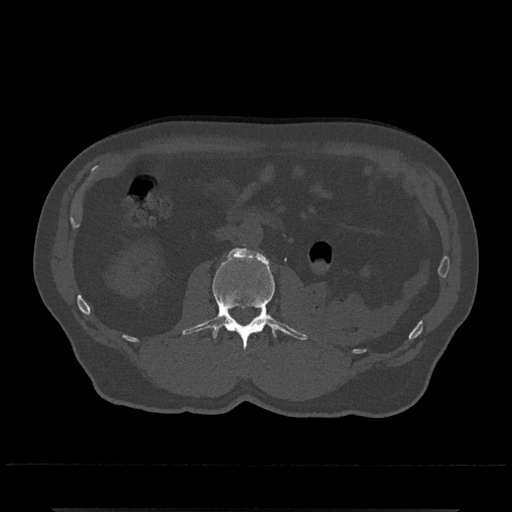
CT including the spine, one axial slice; slice 290 of 797 in the series (ordered by position); 120 kVp; bone window (W 1800 / L 400 HU); 0.5 mm slice thickness; 512 × 512 image matrix, field of view 393 × 393 mm. Patient: male, 67 years. Case-level facts recorded for this patient, not image findings: primary cancer: prostate.
Annotated regions visible in this slice (semi-automatic segmentation, software-assisted and operator-edited):
- L2 vertebra: bounding box [x1, y1, x2, y2] px = [182, 248, 308, 350]